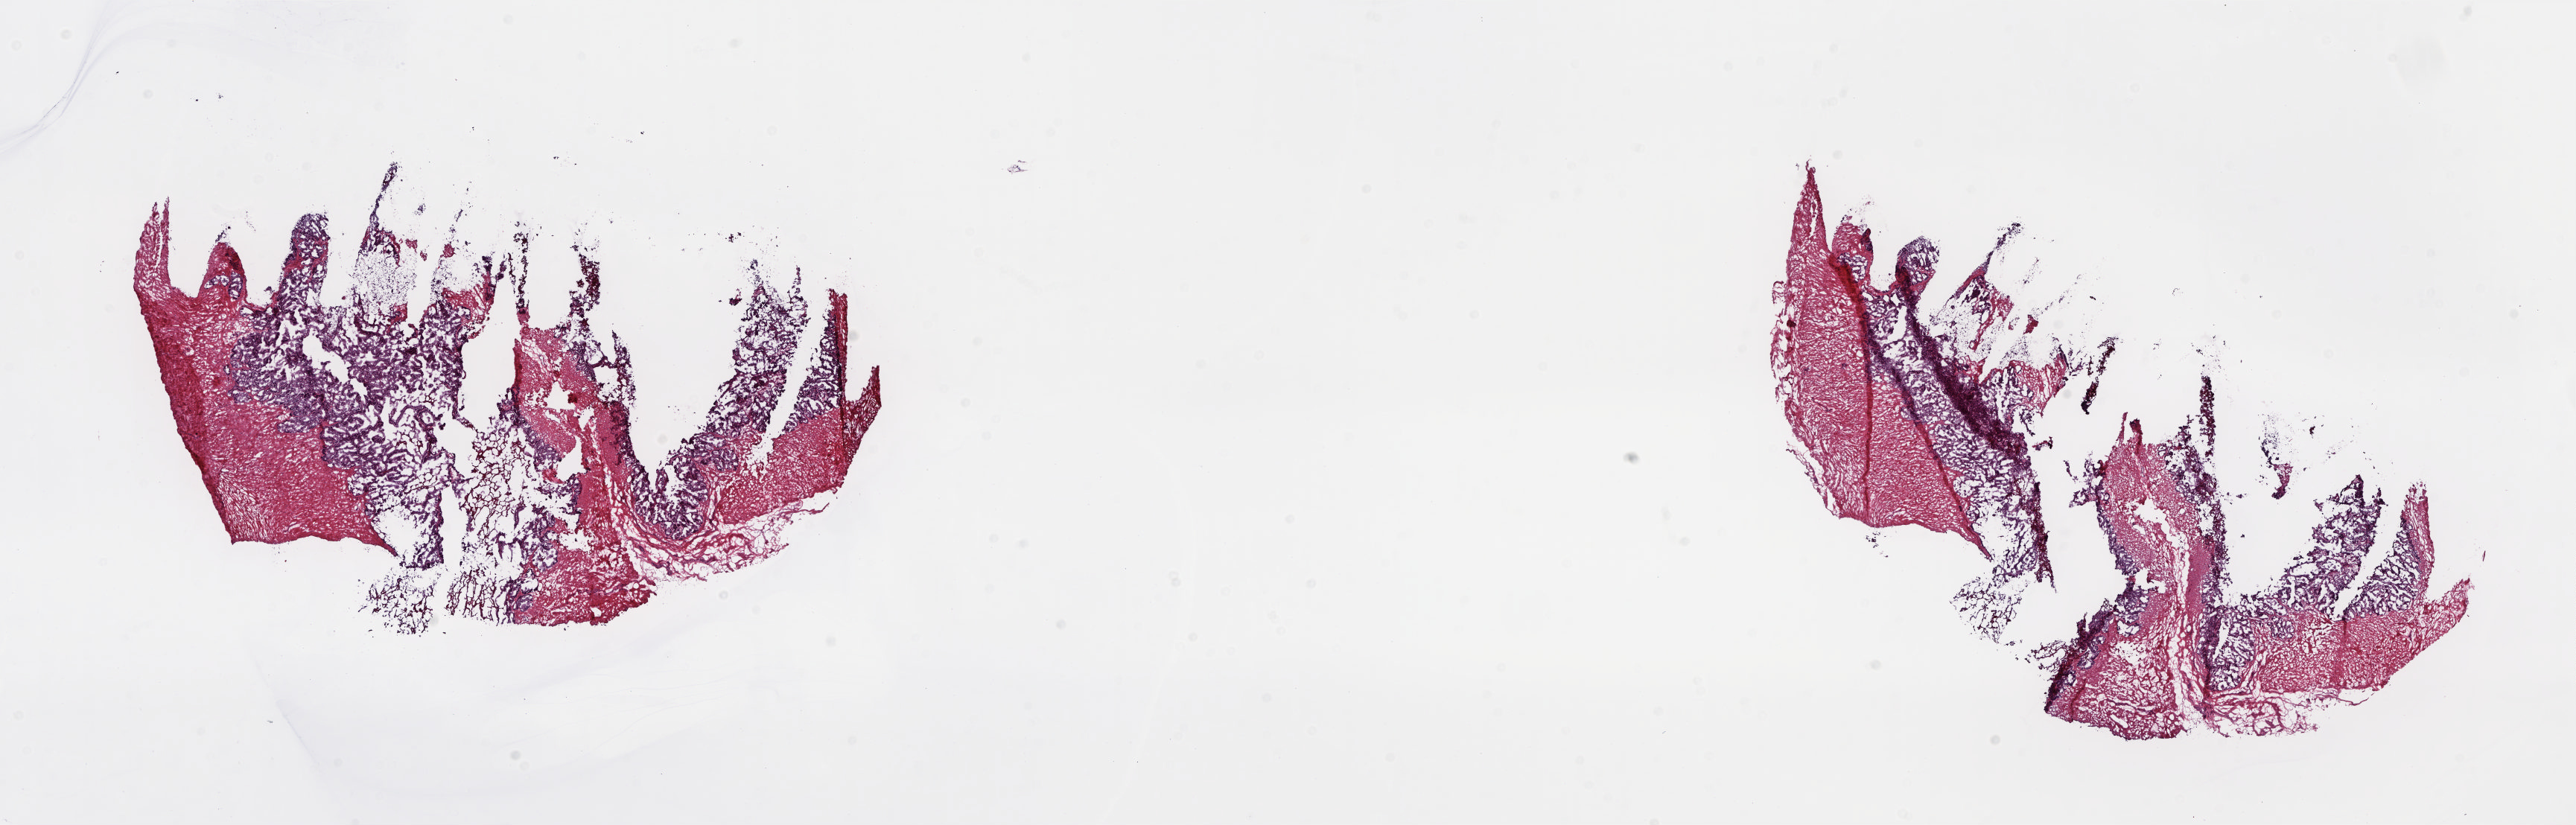
H&E-stained whole-slide image — whole scanned area (about 27.9 x 8.9 mm, slide scanned at 20x) shown as a low-resolution overview. Frozen section from the top of the tissue portion. Solid tissue normal (non-tumour tissue) sample from the prostate. Patient: male, age at initial diagnosis 56 years. Slide review estimates, as recorded: tumour cells 0%, tumour nuclei 0%, normal cells 50%, stromal cells 50%, necrosis 0%. Infiltration values recorded for this section: lymphocyte infiltration 0%, monocyte infiltration 0%, neutrophil infiltration 0%.
* this section: solid tissue normal (non-tumour) sample from the same patient
* patient diagnosis: Adenocarcinoma, NOS (prostate gland)